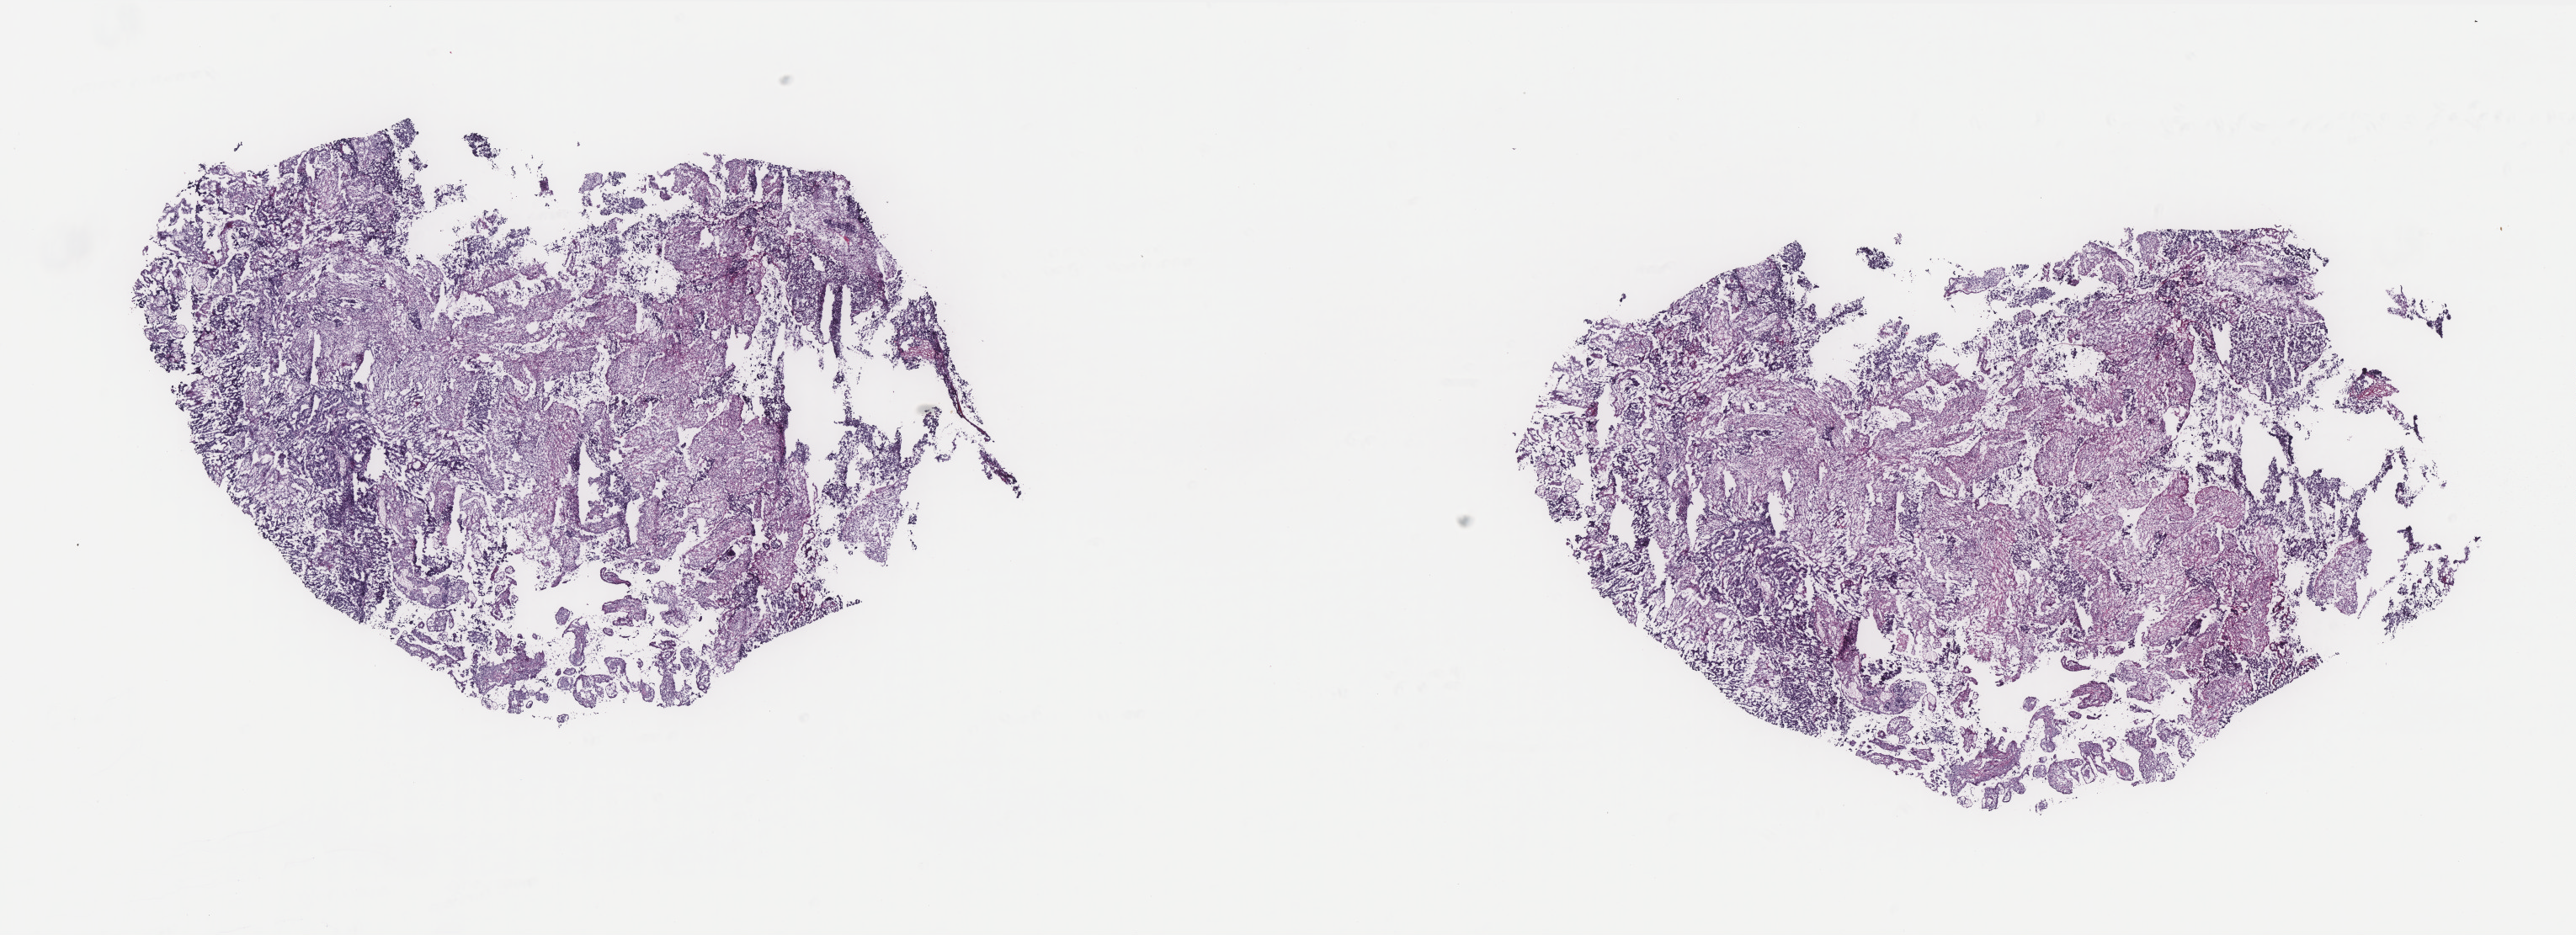
H&E-stained whole-slide image — whole scanned area (about 24.5 x 8.9 mm, slide scanned at 40x) shown as a low-resolution overview, frozen section, primary tumour sample from the uterus. Female, age 74 years at initial diagnosis. Histologic grade: G3 (poorly differentiated). Pathologist review of this section (percent, as recorded): tumour cells 36%, tumour nuclei 40%, normal cells 0%, stromal cells 60%, necrosis 4%. Inflammatory infiltration, as recorded: lymphocyte infiltration 35%, monocyte infiltration 4%, neutrophil infiltration 3%.
- diagnosis: Endometrioid adenocarcinoma, NOS (endometrium)
- FIGO stage: IVB